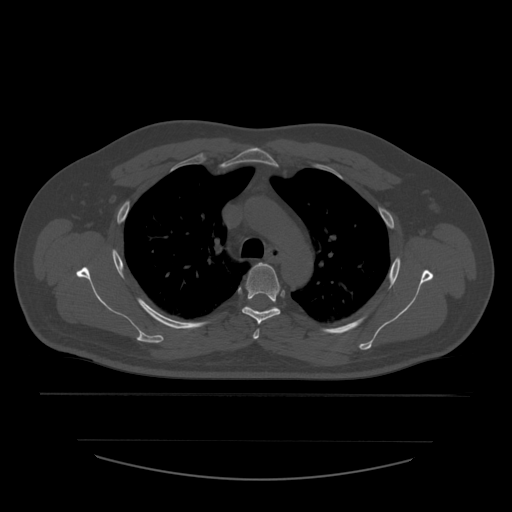
CT including the spine, one axial slice. Position 417 of 532 along the scan axis. Reconstruction kernel STANDARD. 120 kVp. Bone window (W 1800 / L 400 HU). 512 × 512 image matrix. Patient age 44 years. Case-level facts recorded for this patient, not image findings: primary cancer: soft tissue sarcoma.
Outlined on this slice (semi-automatic segmentation, software-assisted and operator-edited):
- T3 vertebra: bounding box [x1, y1, x2, y2] px = [253, 321, 260, 340]
- T4 vertebra: [242, 263, 281, 324]
- T5 vertebra: [245, 306, 277, 311]